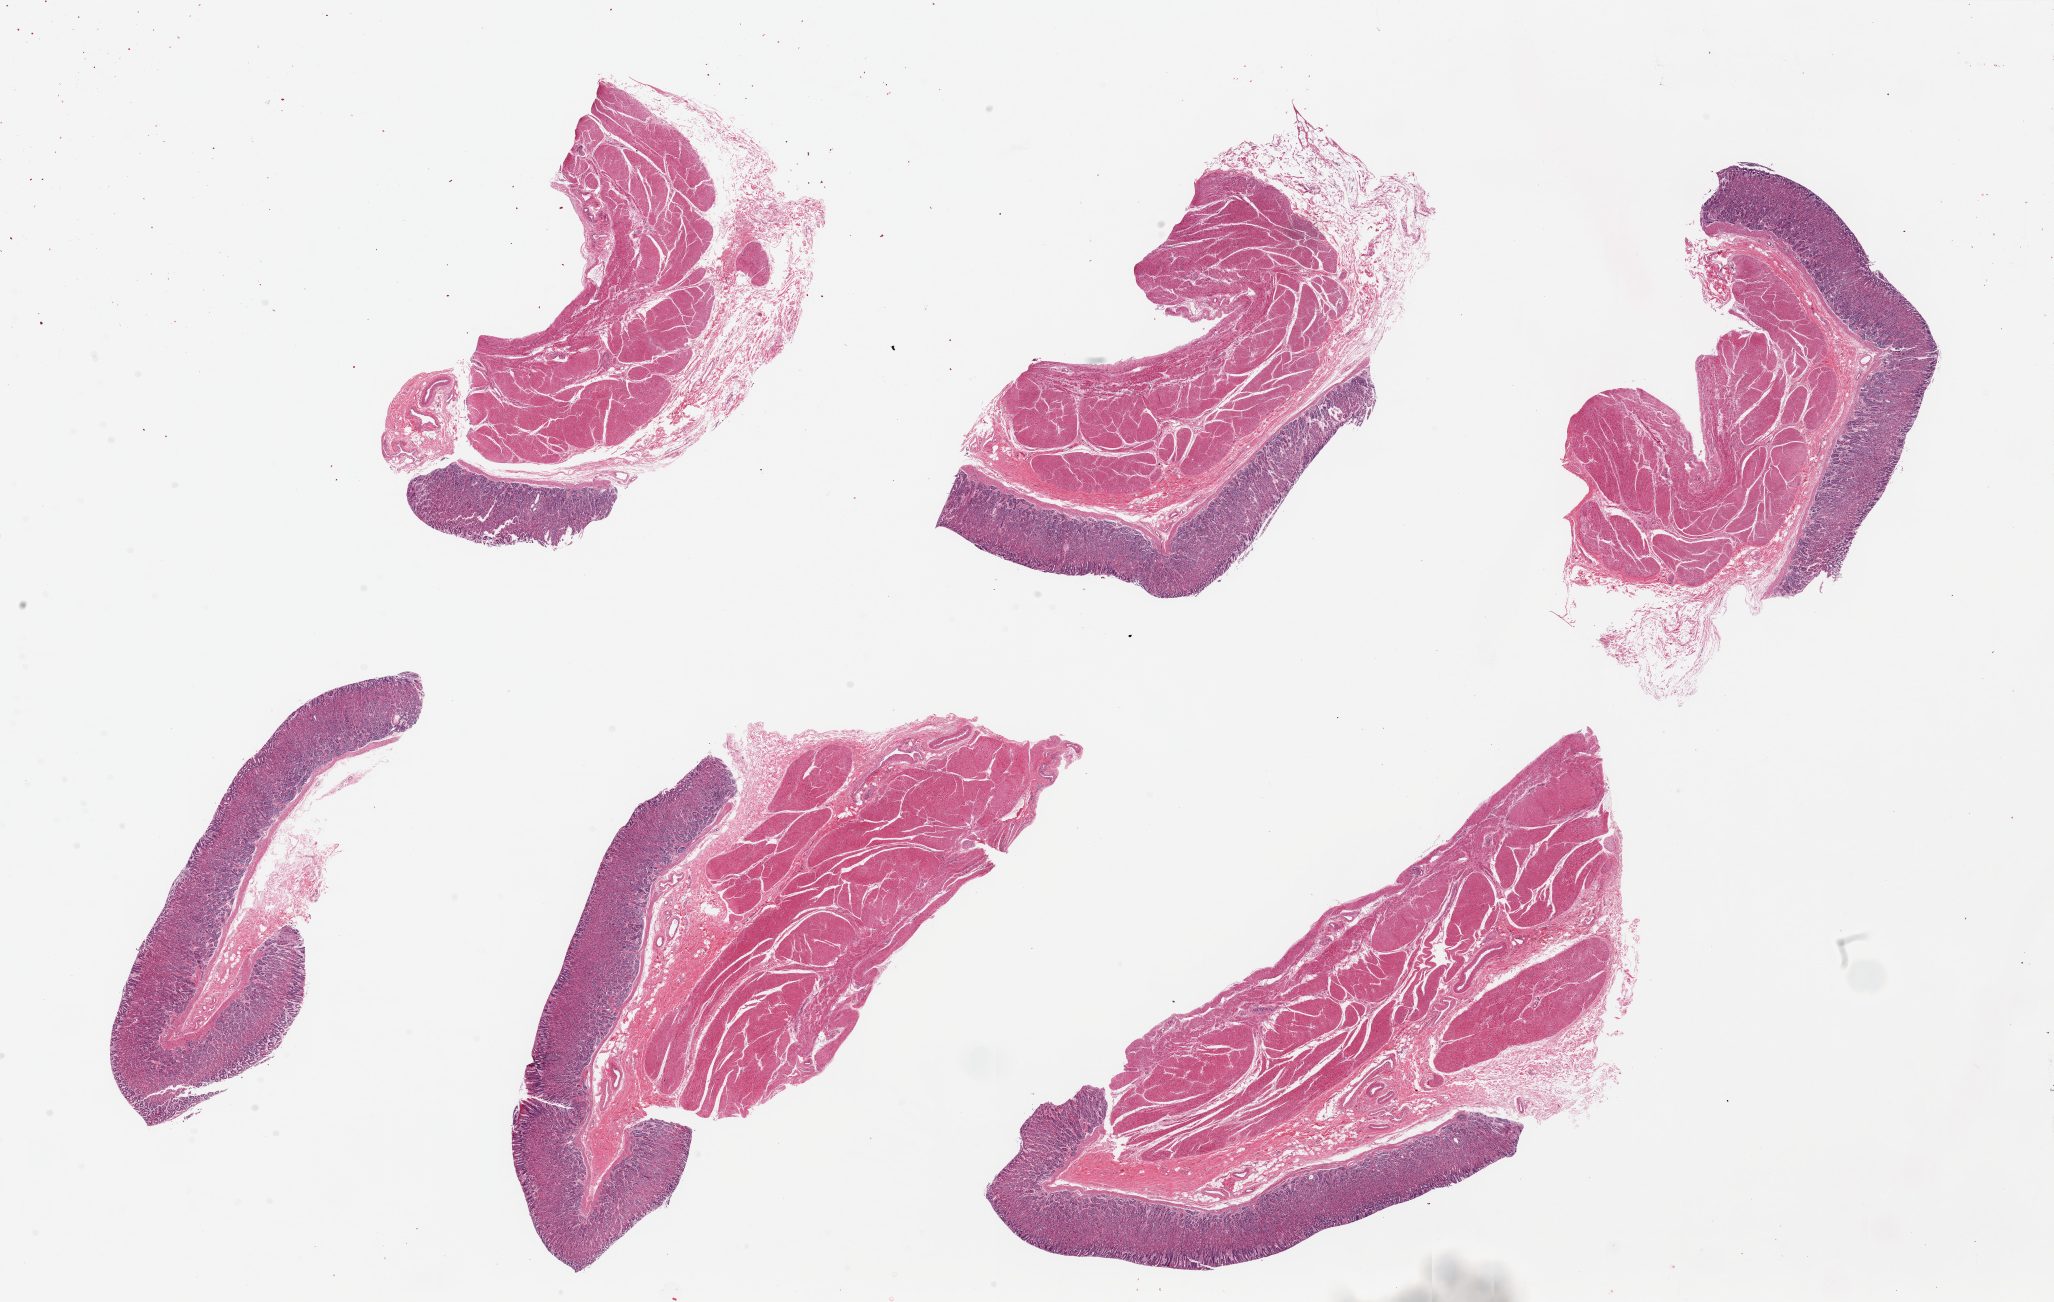
Haematoxylin and eosin whole-slide image, whole scanned area (about 32.5 x 20.6 mm) shown as a low-resolution overview, PAXgene-fixed paraffin-embedded (PFPE) section, sampled site (target tissue): stomach, tissue donor sample.
Review note (as recorded): 6 pieces, up to 12x5mm; Good well preserved mucosa.